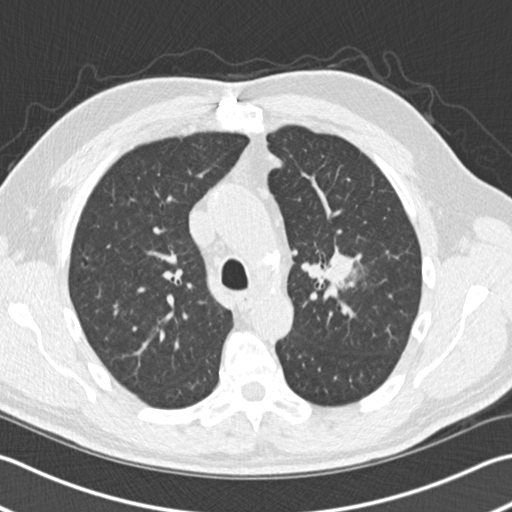
Low-dose screening chest CT, one axial slice. Slice 107 of 153 in the series (ordered by position). Reconstruction kernel B30f. Lung window (W 1500 / L -600 HU). 2 mm slice thickness. 512 × 512 image matrix, field of view 346 × 346 mm.
Outlined on this slice (expert manual segmentation):
- lesion 1 (tumor, upper lobe of left lung): bounding box <324,253,353,284> (left, top, right, bottom; pixels)